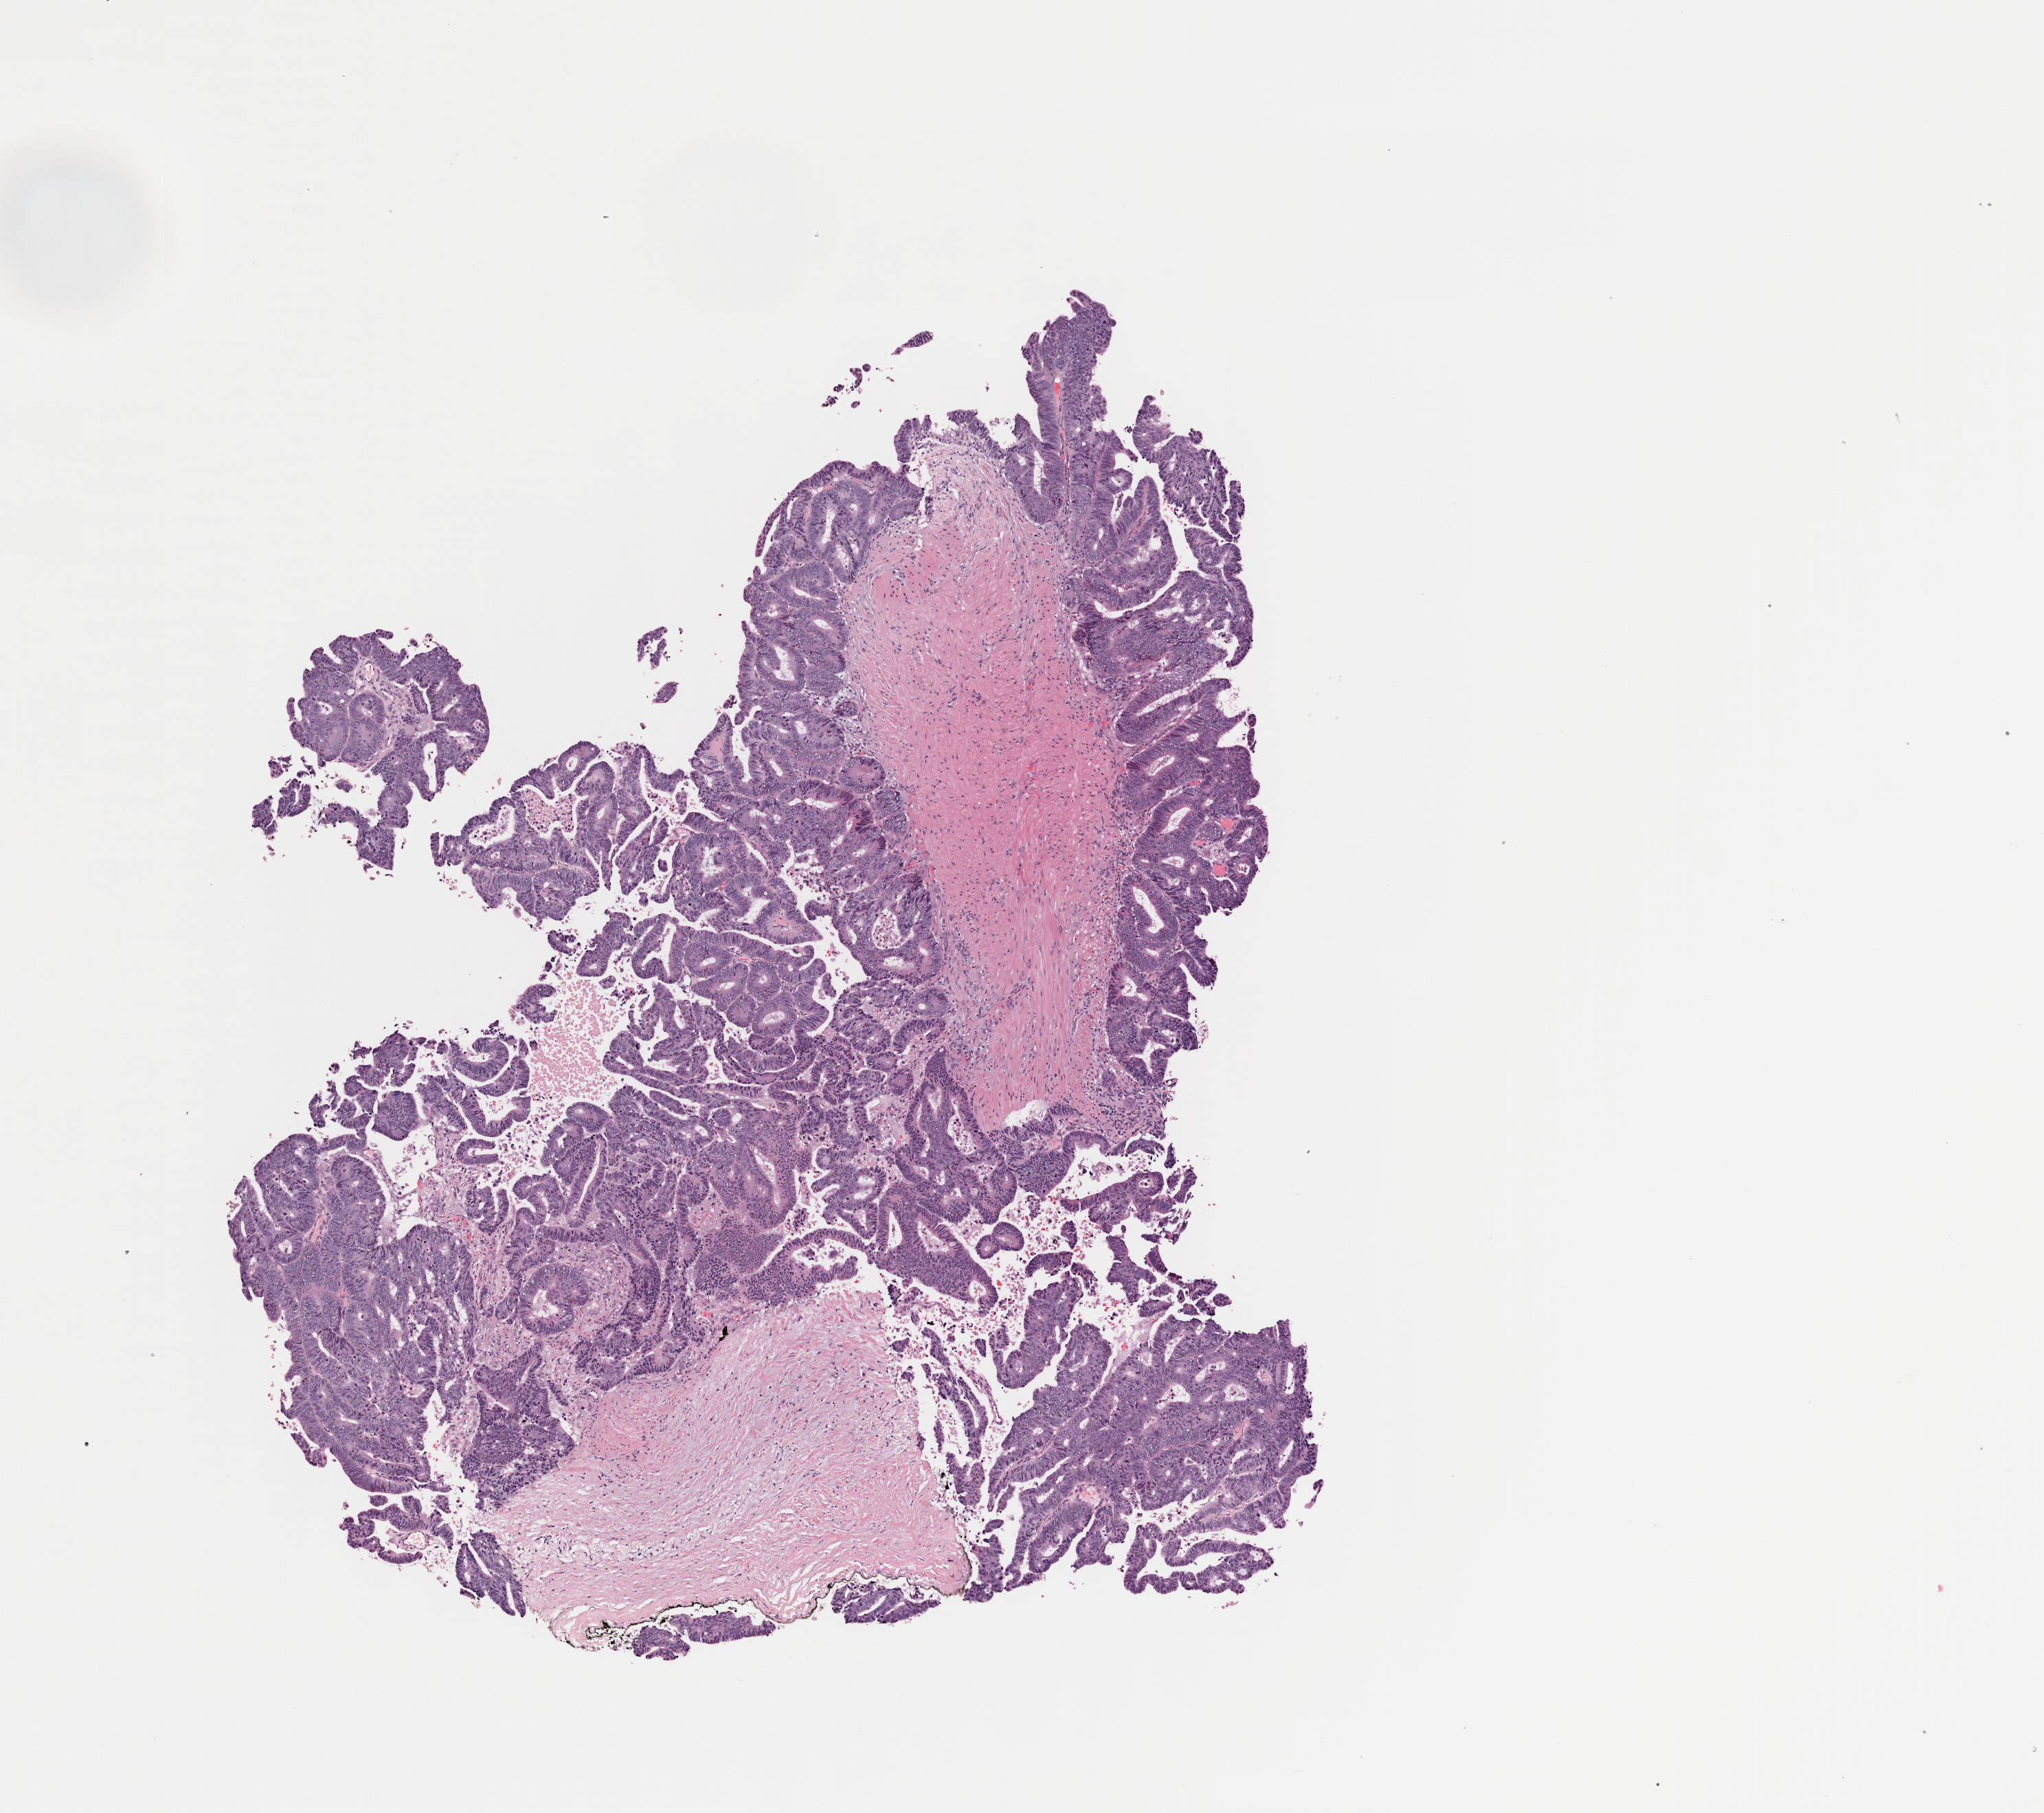
H&E-stained whole-slide image — low-resolution overview of the scanned area, about 5.9 x 5.2 mm; frozen section; colon, primary tumour sample. Patient: male, age at initial diagnosis 82 years. Composition of this section per pathologist review: tumour cells 53%, tumour nuclei 80%.
Diagnosis: Adenocarcinoma, NOS (ascending colon).